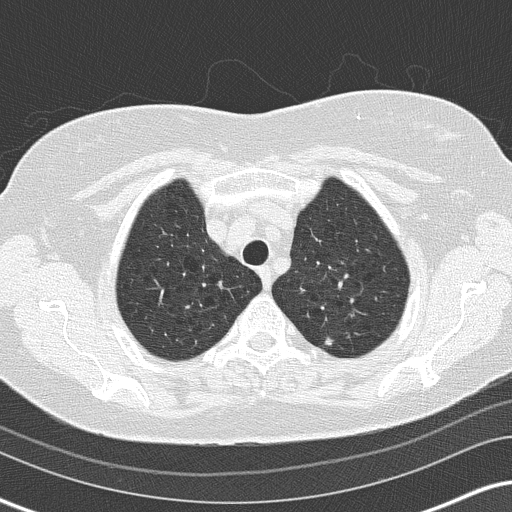
Chest CT (low-dose screening protocol), one axial image, baseline annual screen, lung window (W 1500 / L -600 HU), 2 mm slice thickness, slice 27 of 159 in the series, 512 × 512 image matrix. Female, age 65 years at enrolment. Former smoker at enrolment.
Lesion marked by an expert reader, box from (x=307, y=326) to (x=347, y=359) px. The exam's reader record, not a measurement of the box and not confirmed to be the same lesion: non-calcified nodule or mass ≥4 mm, left upper lobe, 6 × 5 mm, soft tissue attenuation. Official screen result: positive, change unspecified: nodule(s) >= 4 mm or enlarging nodule(s), mass(es), or other non-specific abnormalities suspicious for lung cancer. Later outcome: lung cancer diagnosed 800 days after this screen (after the third annual screen) — adenocarcinoma, NOS, left upper lobe, moderately differentiated (G2), stage IA (AJCC 6th edition), 8 mm at pathology.